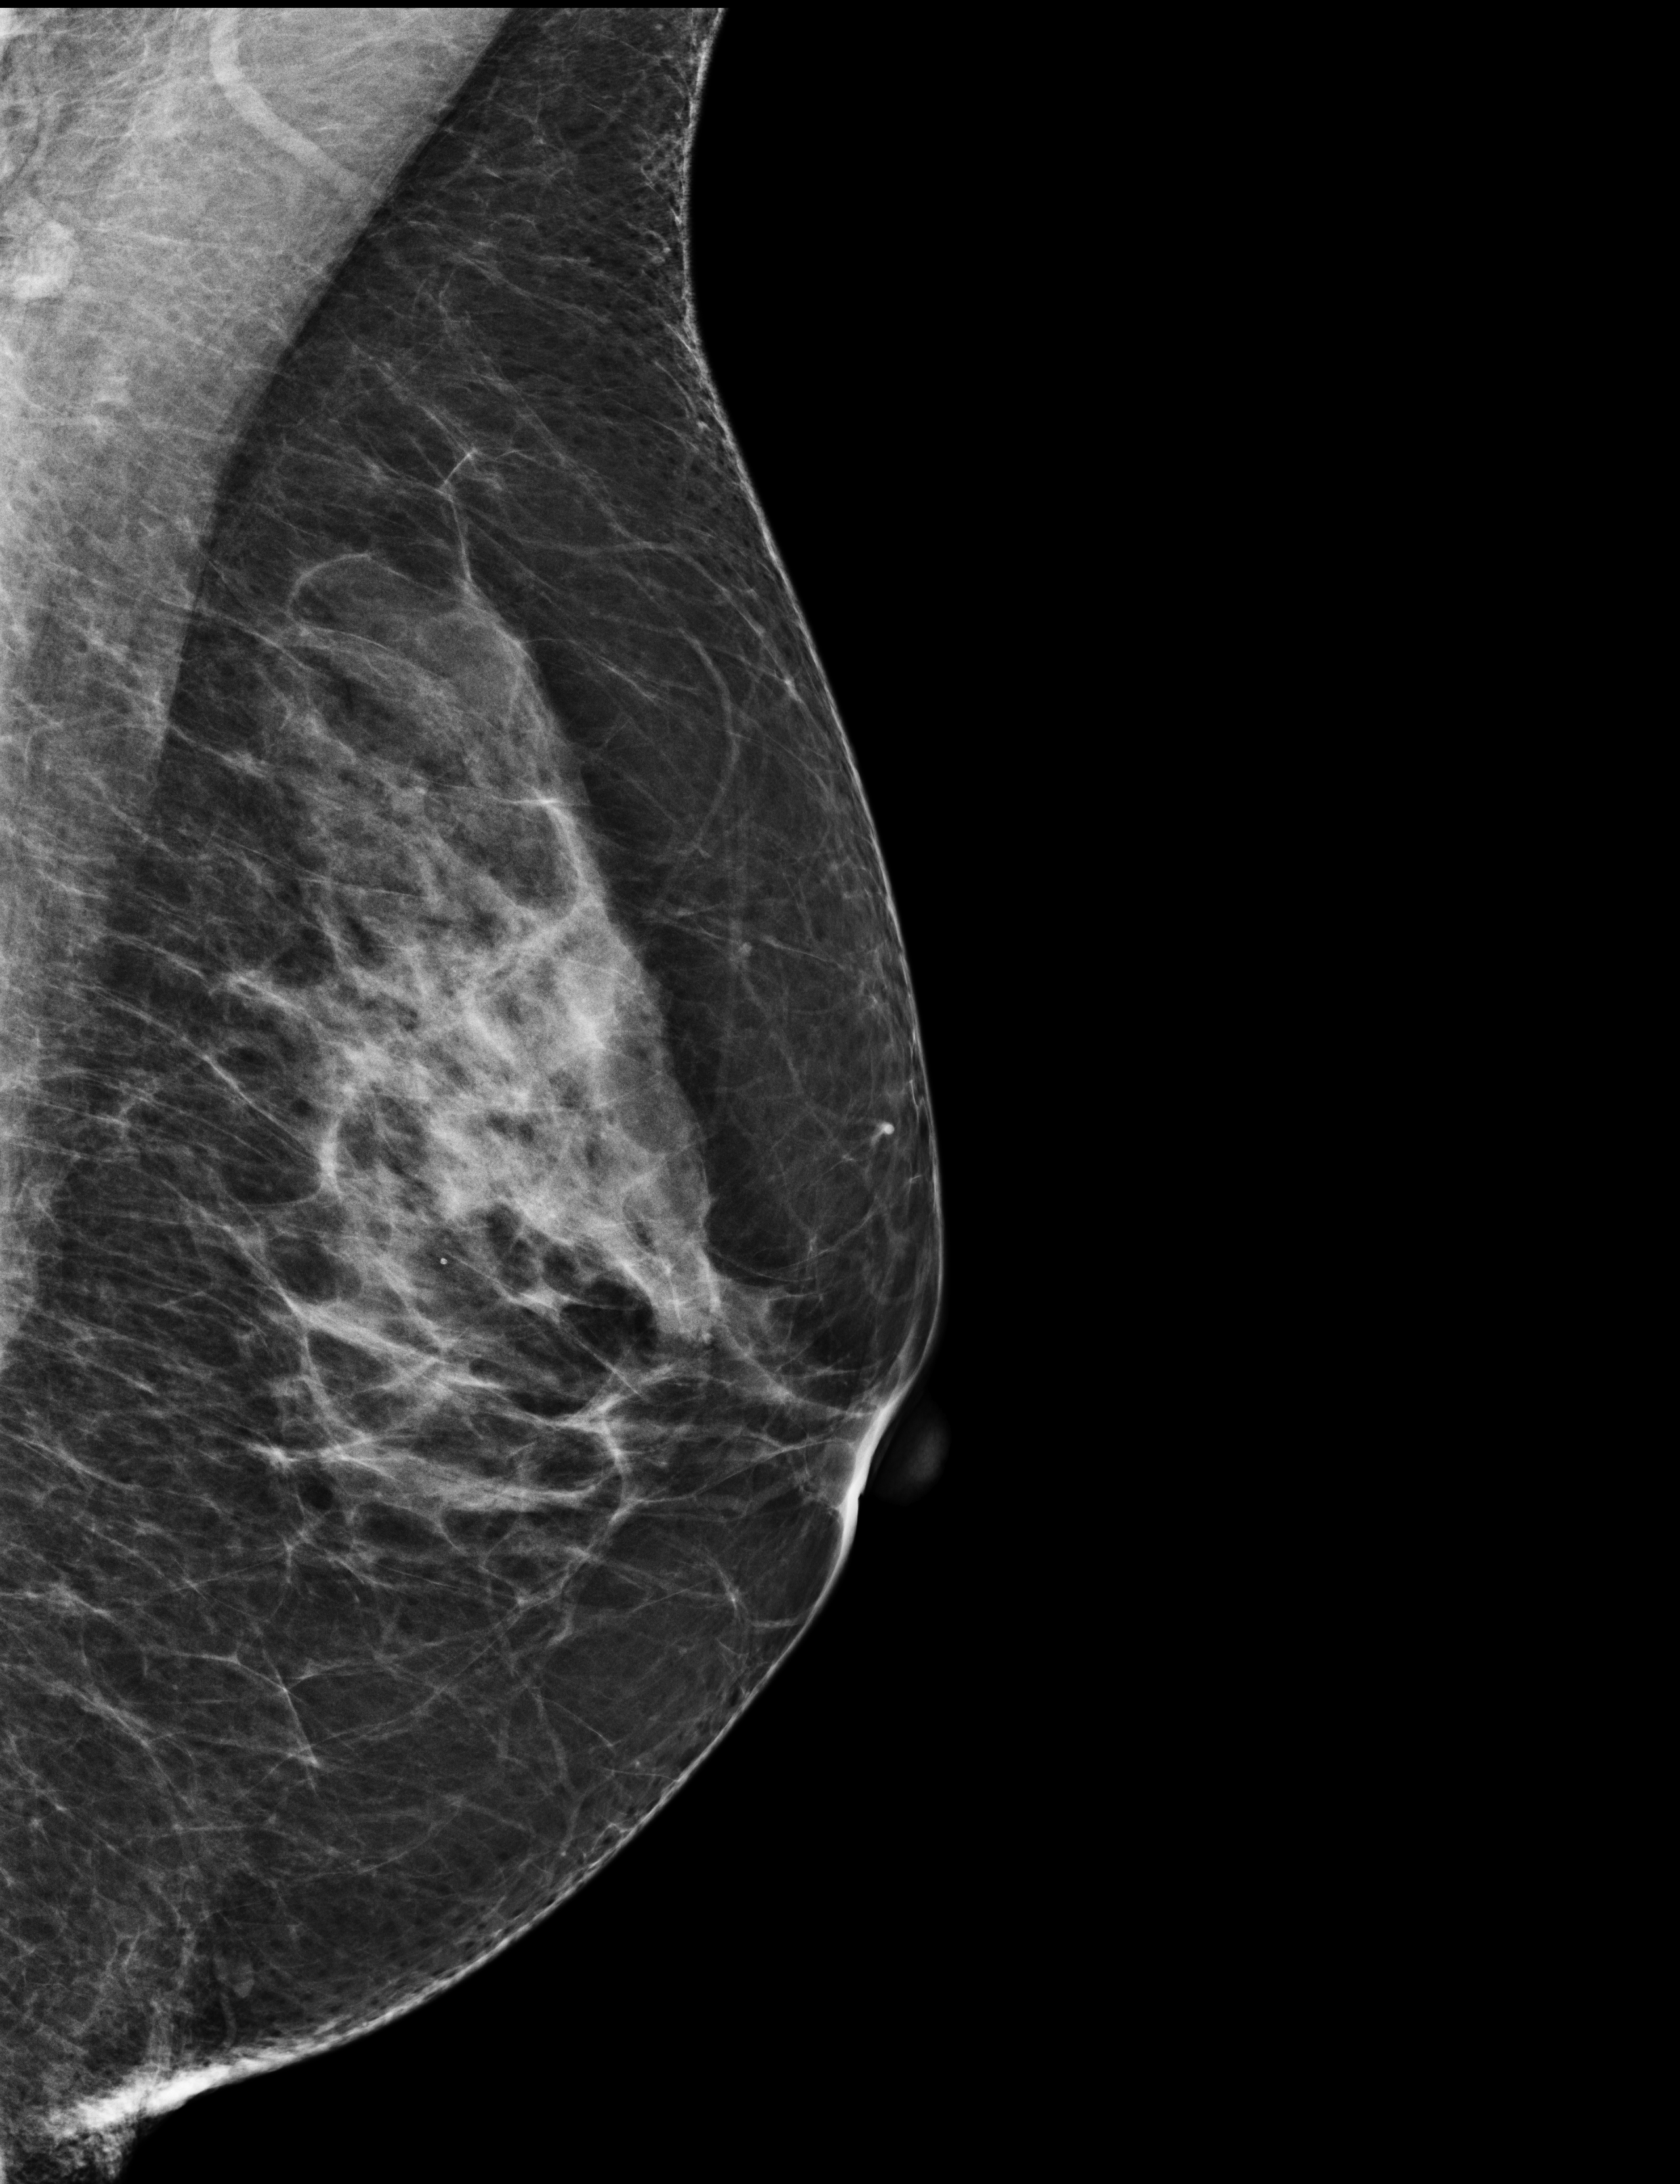
Screening examination; compressed breast thickness 66 mm. Female patient, age 63 years.
Image type: full-field digital mammogram. Breast: left. Projection: medio-lateral oblique projection.